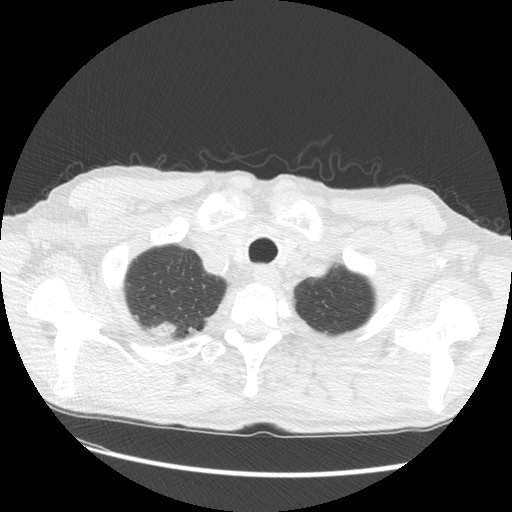
Low-dose screening chest CT, one axial slice; slice 124 of 133 in the series (ordered by position); reconstruction kernel STANDARD; 120 kVp; lung window (W 1500 / L -600 HU); 2.5 mm slice thickness; 512 × 512 image matrix, field of view 360 × 360 mm.
Annotated regions visible in this slice (expert manual segmentation):
- lesion 2 (tumor, upper lobe of right lung): bounding box [x1, y1, x2, y2] px = [149, 321, 177, 338]